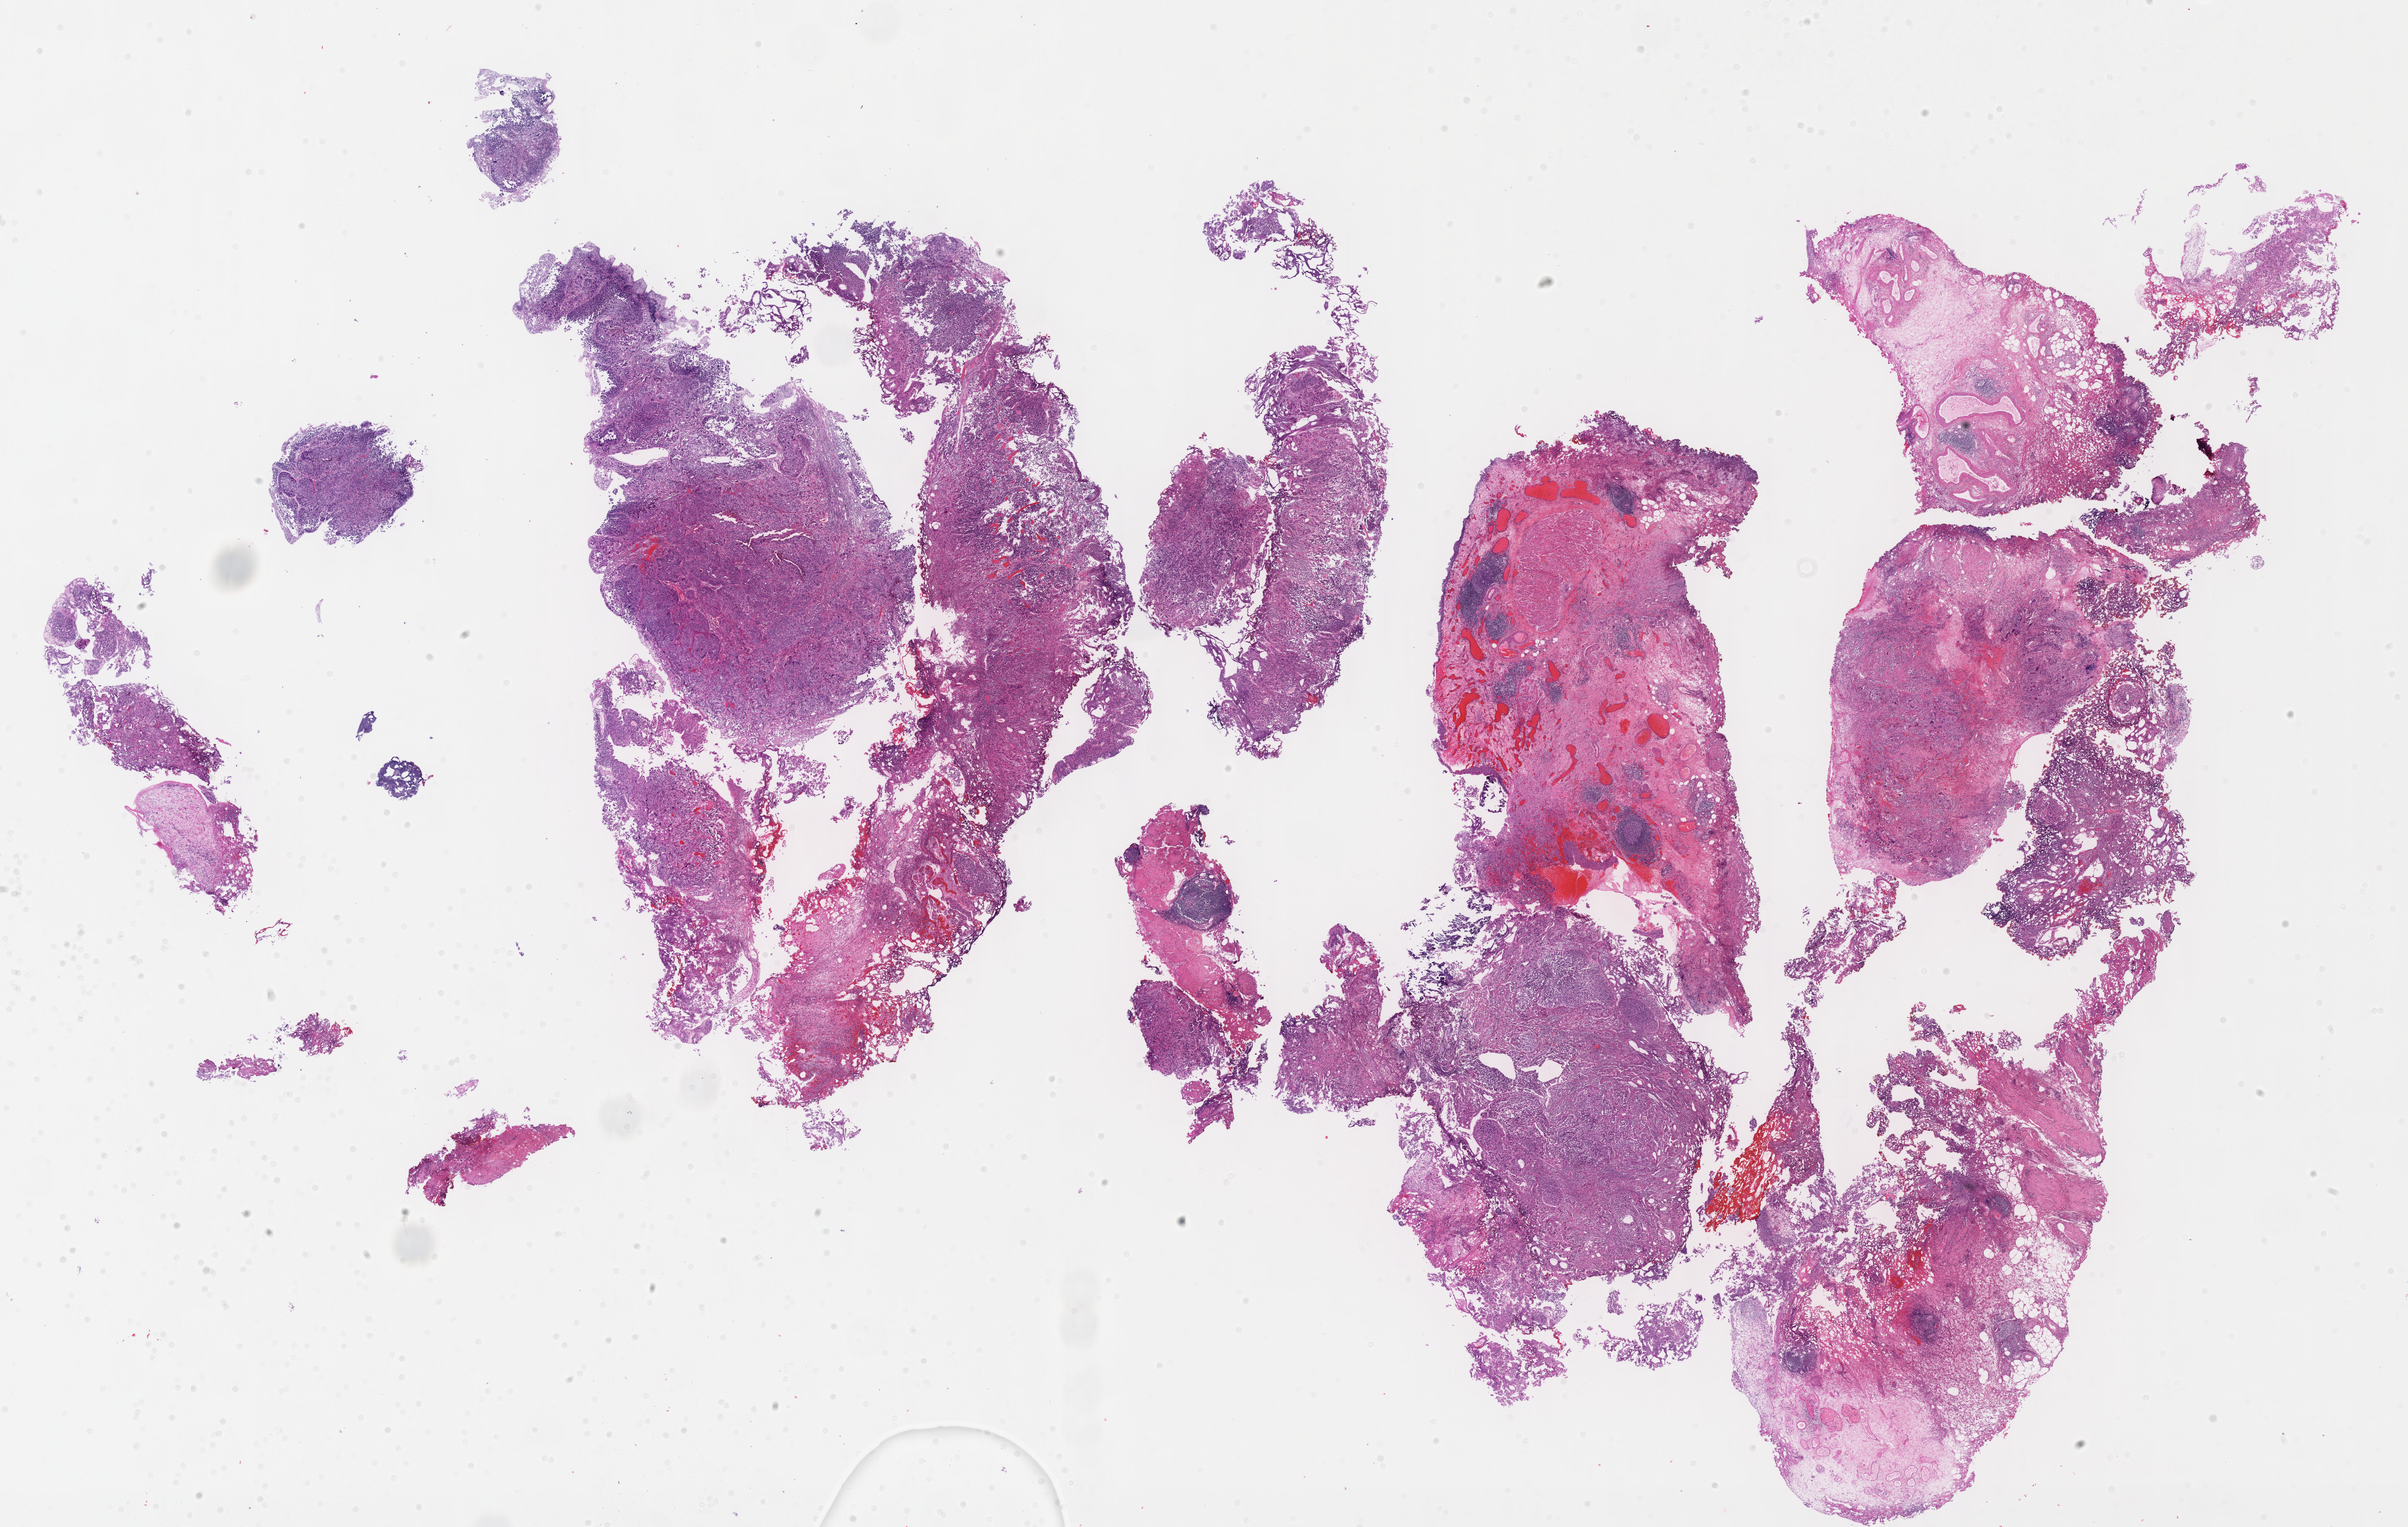
Whole-slide histology image, H&E-stained — shown as a low-resolution overview of the whole scanned area (about 31.7 x 20.1 mm, slide scanned at 40x). Formalin-fixed paraffin-embedded (FFPE) diagnostic section. Primary tumour sample from the bladder. Female, age 75 years at initial diagnosis. Histologic grade: high grade.
Lymph nodes positive (case pathology): 0 of 25 examined. Pathologic diagnosis: Transitional cell carcinoma. AJCC pathologic stage: II (6th edition).